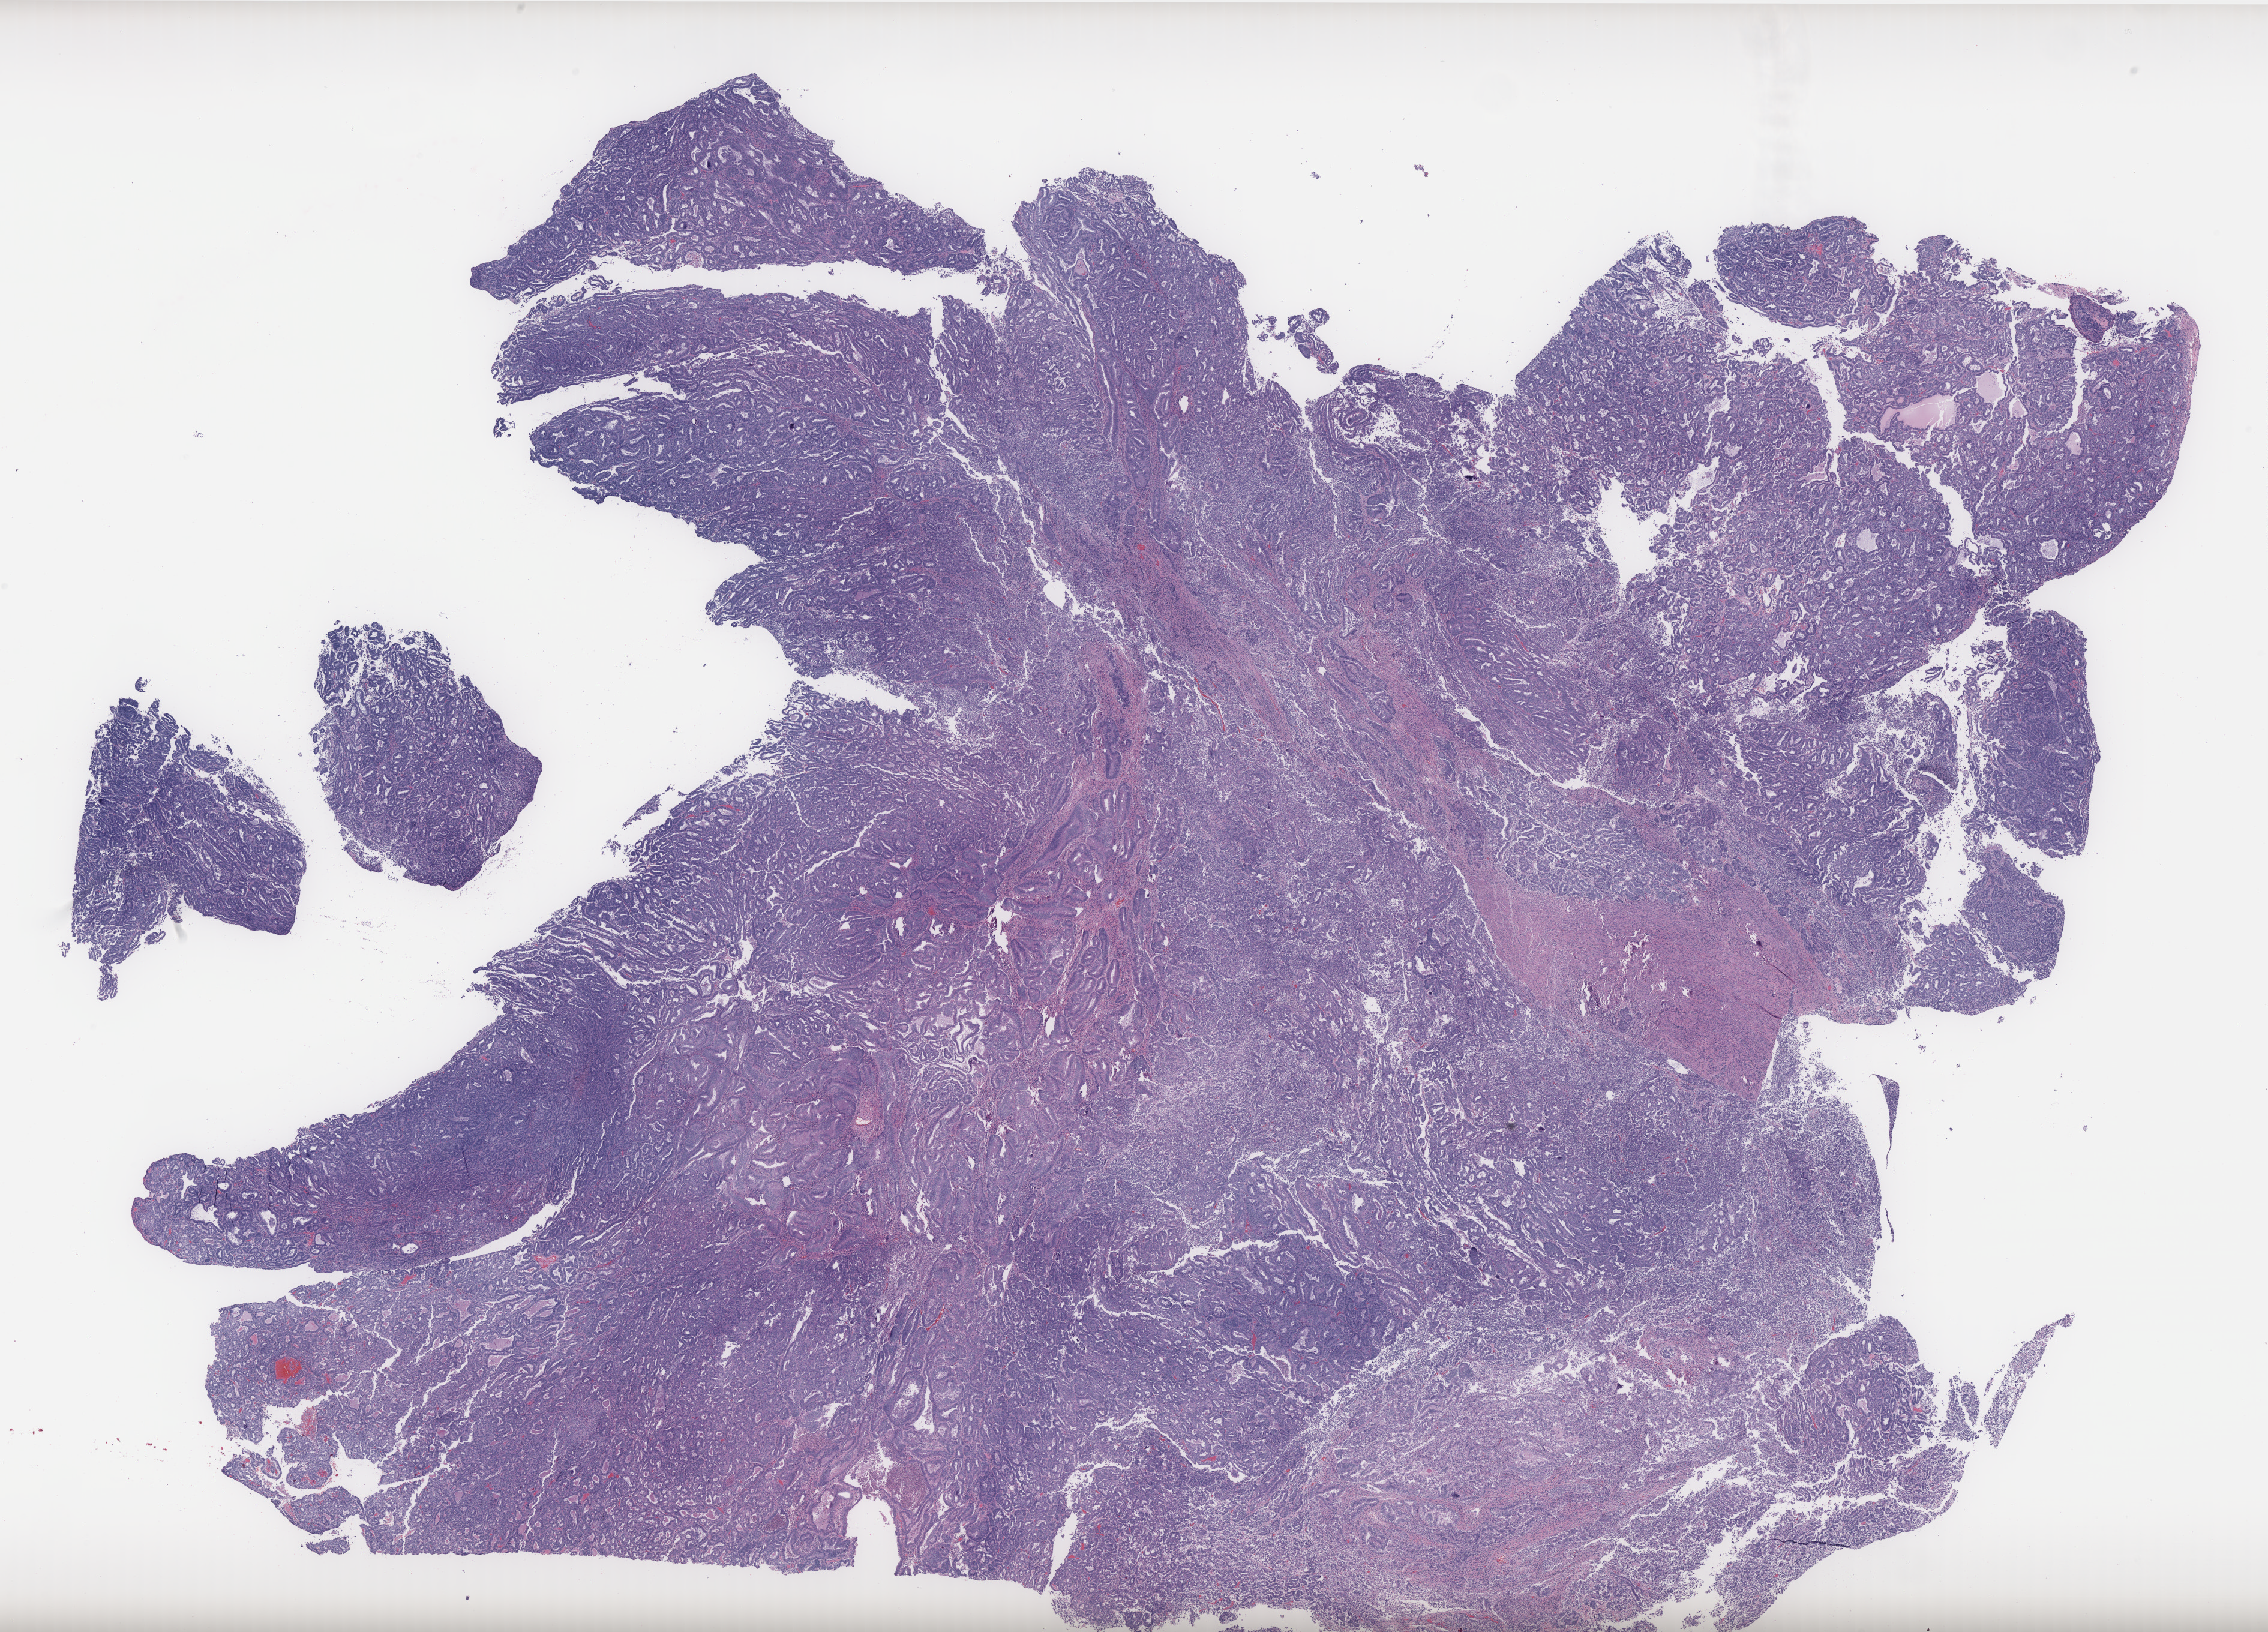
Whole-slide histology image, Hematoxylin and eosin (H&E) stained — low-resolution overview of the scanned area, about 30.3 x 21.8 mm (acquisition: 40x scan); formalin-fixed paraffin-embedded (FFPE) diagnostic section; sample: primary tumour, uterus. Patient: female, age at initial diagnosis 66 years. Histologic grade: G1 (well differentiated).
• pathologic diagnosis: Endometrioid adenocarcinoma, NOS
• FIGO stage: IA